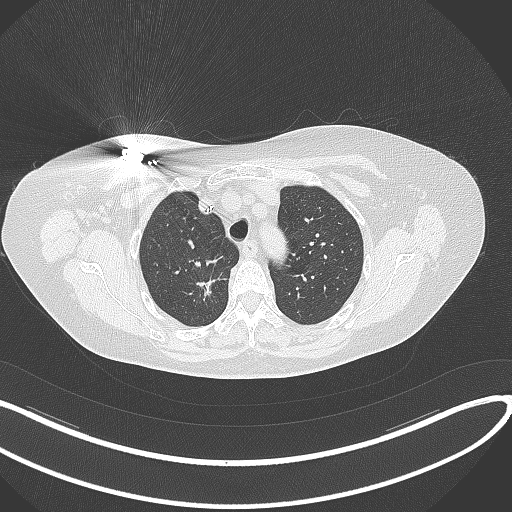
Chest CT, one axial slice; slice 264 of 316 in the series (ordered by position); lung window (W 1500 / L -600 HU); 512 × 512 image matrix, field of view 400 × 400 mm. Patient: female, 72 years. Case-level facts recorded for this patient, not image findings: clinical TNM (as recorded): T1c N0 M0.
Structures marked on this image (bounding box drawn by a radiologist):
- lung tumour (recorded histology: adenocarcinoma): bounding box <196,271,225,299> (left, top, right, bottom; pixels)